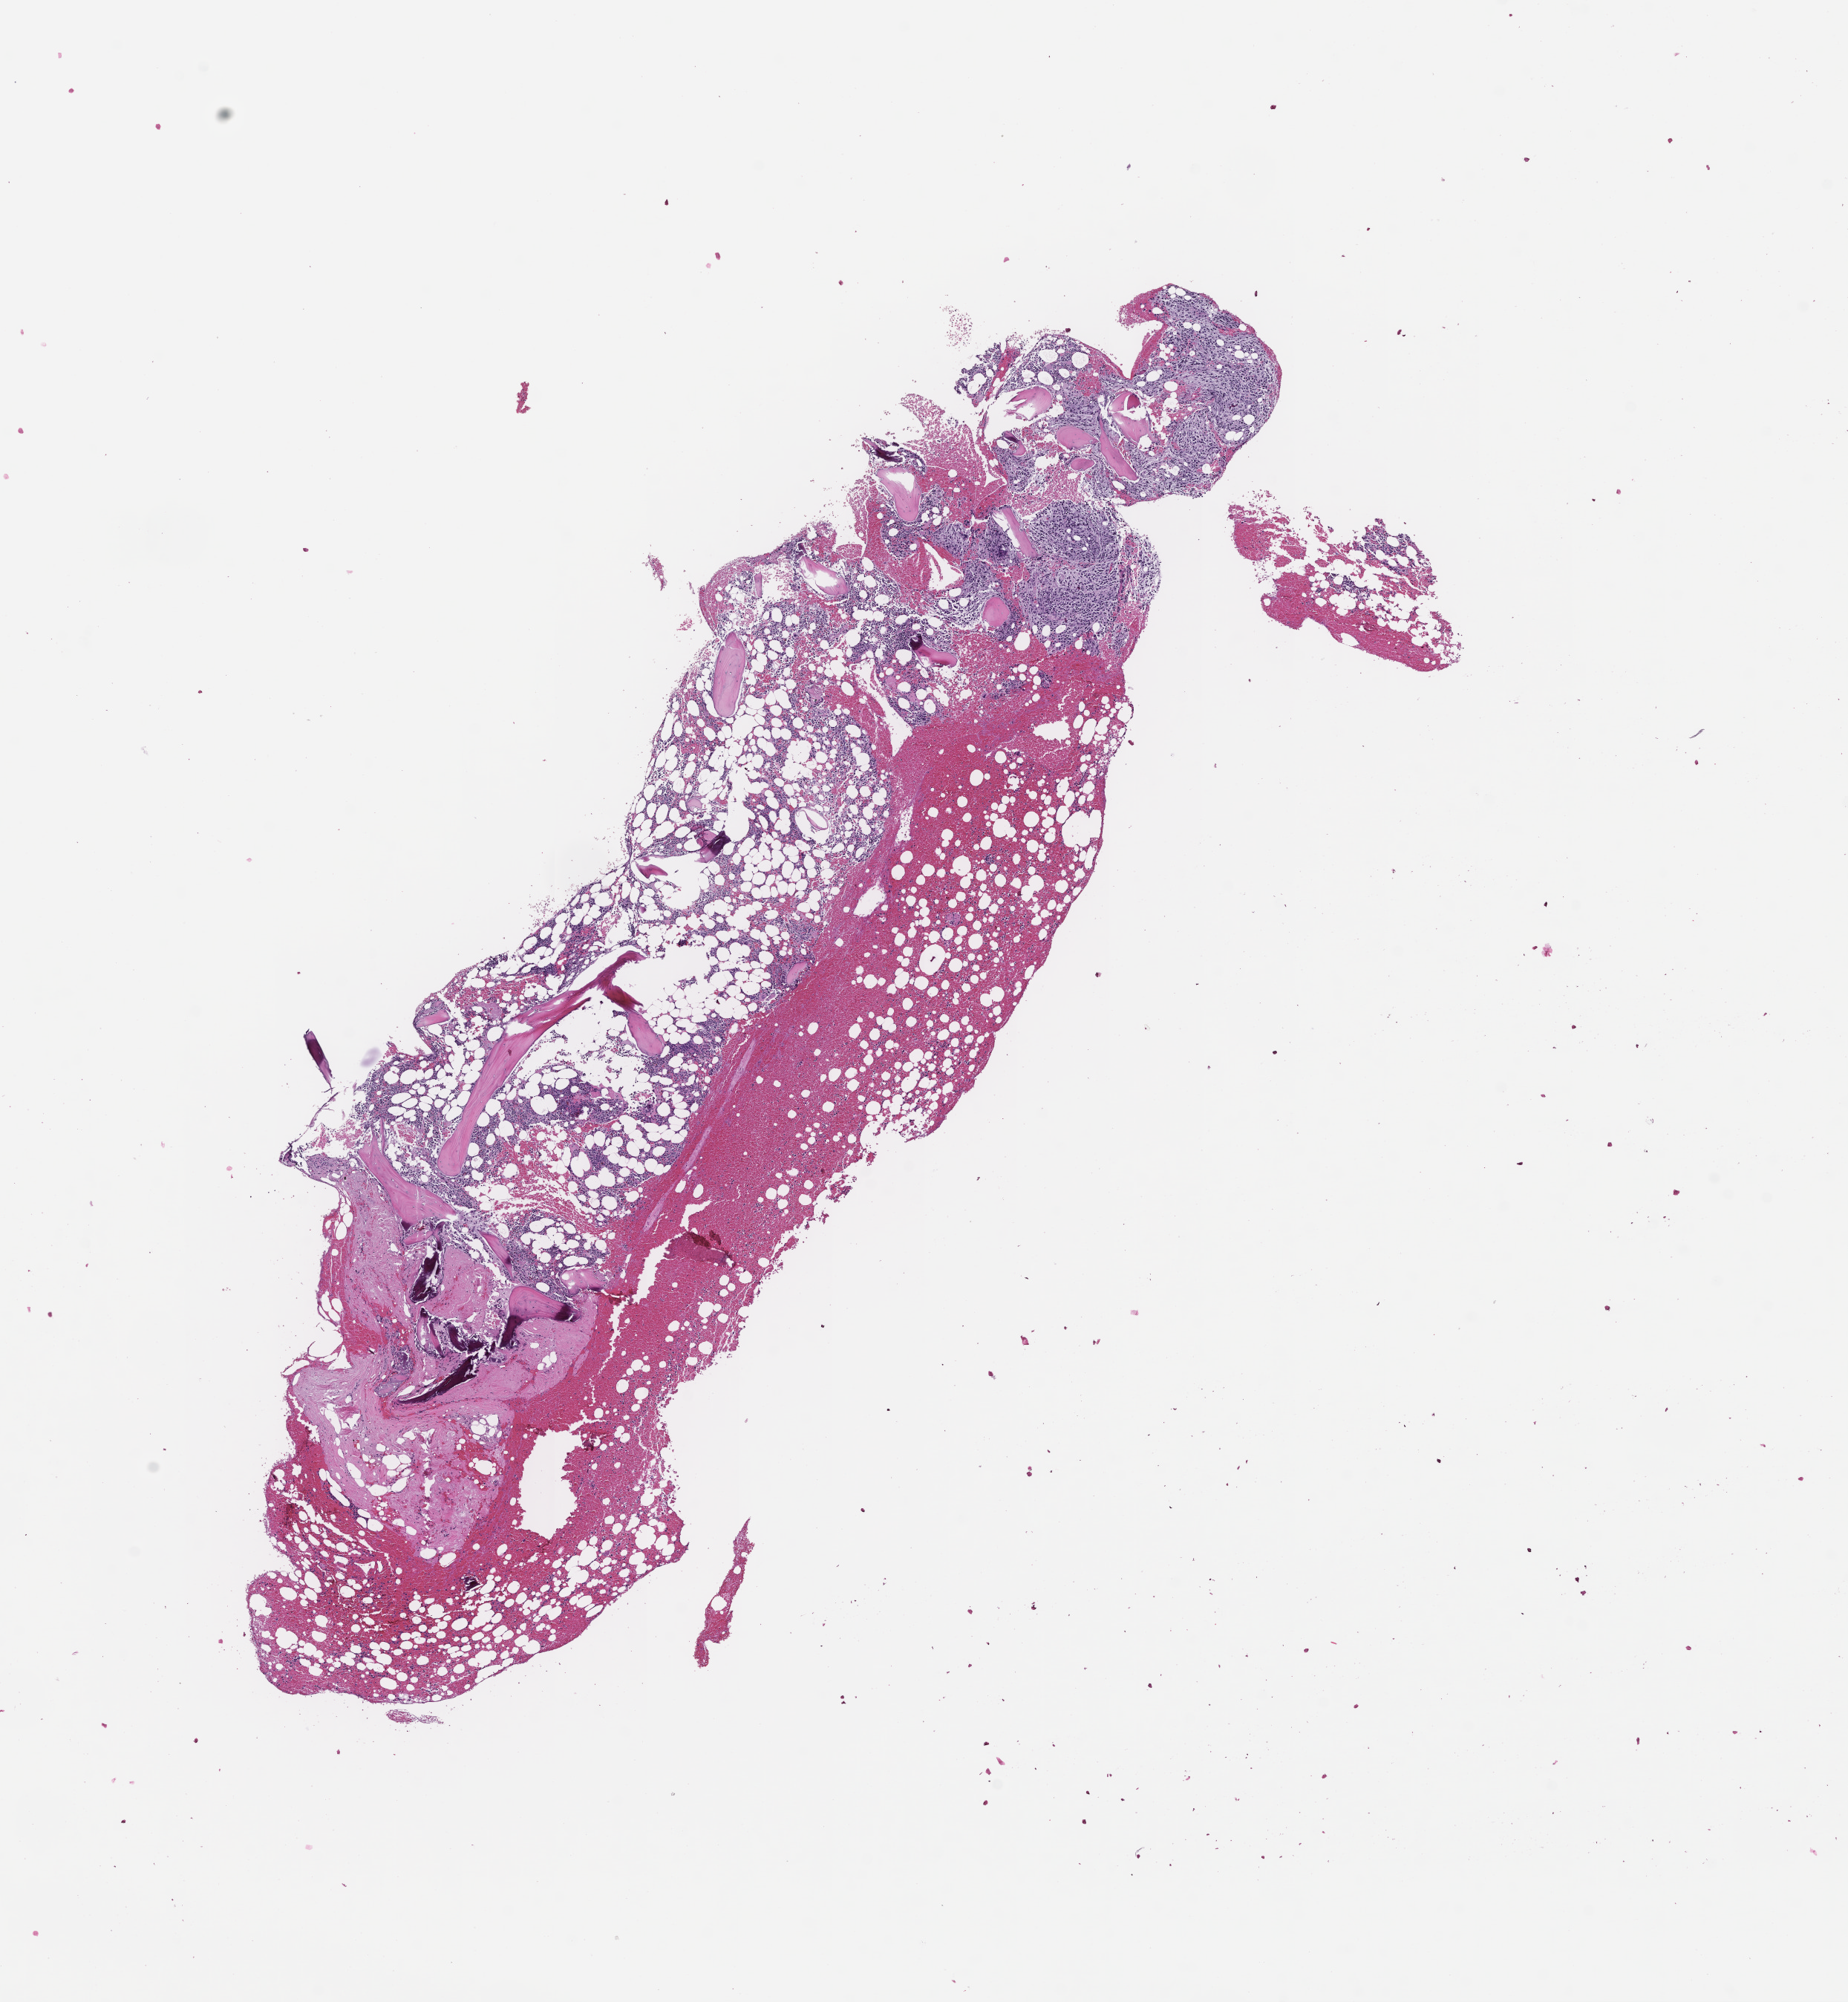
H&E whole-slide image — a low-resolution overview of the entire scanned area, about 10.1 x 10.9 mm, FFPE section, tissue site: bone marrow, collected at disease progression. Patient sex: male.
This section: primary tumour tissue. Diagnosis: Plasma Cell Myeloma.